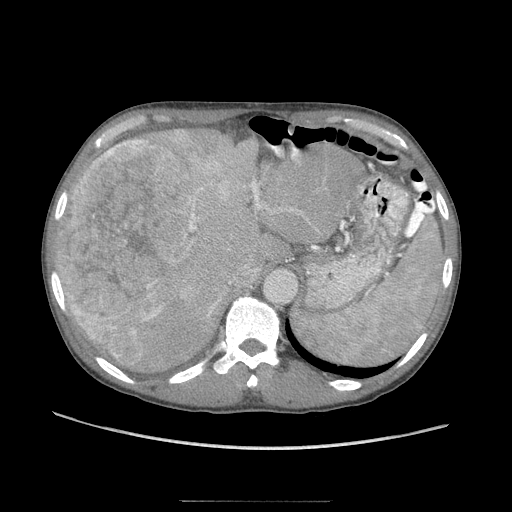
Contrast-enhanced abdominal CT (liver protocol), one axial slice; position 69 of 103 along the scan axis; 120 kVp; soft-tissue window (W 400 / L 40 HU); 2.5 mm slice thickness; 512 × 512 image matrix. Case-level facts recorded for this patient, not image findings: diagnosis: hepatocellular carcinoma (patient treated with transarterial chemoembolisation; whether this scan precedes or follows treatment is not stated here); TNM stage (as recorded): Stage-IIIA; Child-Pugh class: A; tumour differentiation: moderately differentiated.
Outlined on this slice (semi-automatically segmented with operator editing):
- liver parenchyma outside the tumour (the mass and vessels are separate outlines, so this box may not span the whole liver): bounding box <56,128,356,370> (left, top, right, bottom; pixels)
- mass: <60,140,190,368>
- liver vessels: <130,215,198,334>